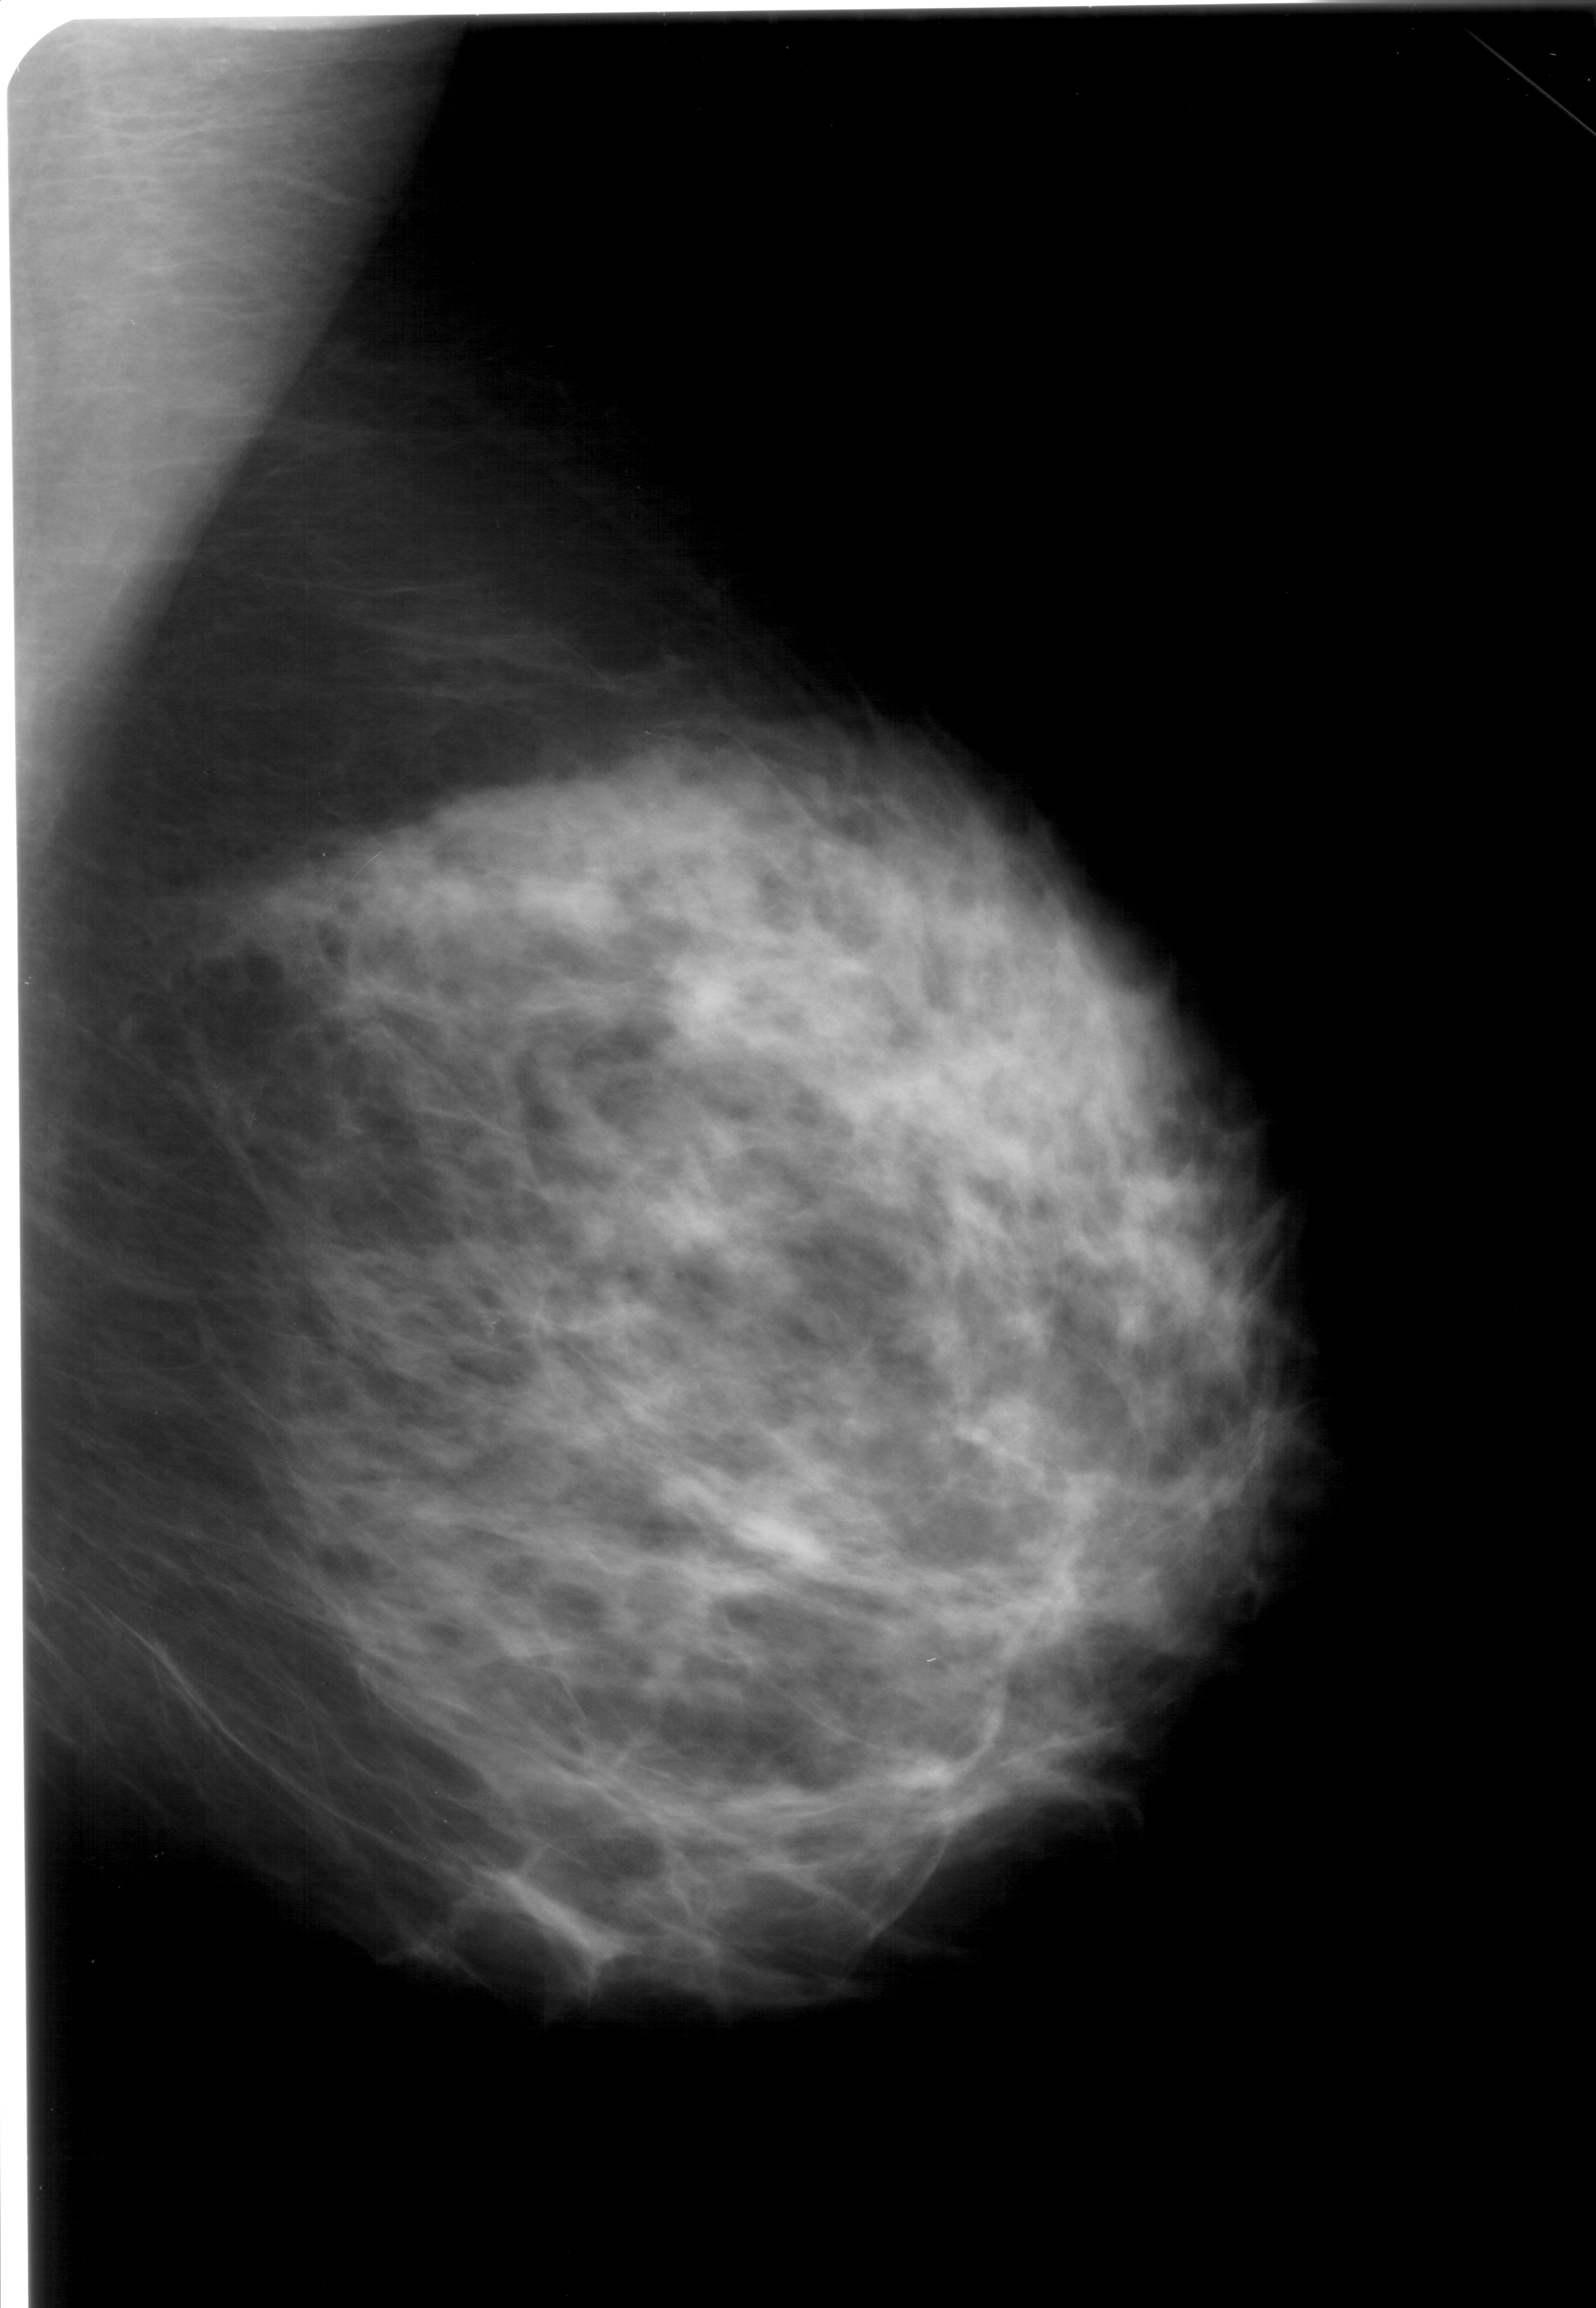
Digitized screen-film mammogram. Right breast. Mediolateral oblique (MLO) view. Breast composition: heterogeneously dense (BI-RADS density category 3 of 4). 1596 × 2308 image matrix.
Expert-marked regions of interest on this film, with their recorded descriptors:
- calcifications, morphology pleomorphic, distribution clustered; BI-RADS assessment category 4; pathology (as recorded): benign: bounding box <463,1301,520,1351> (left, top, right, bottom; pixels)